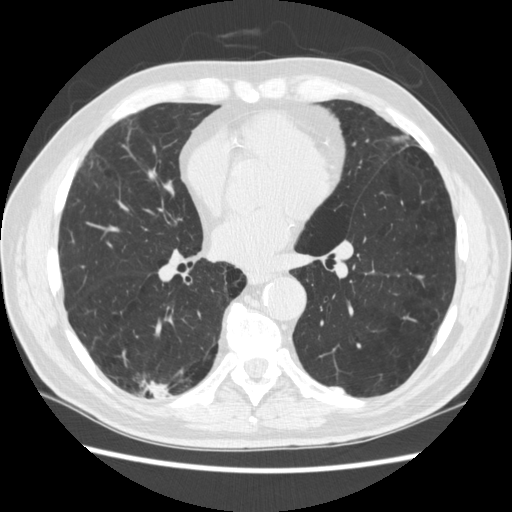
Axial slice from a low-dose chest CT screening exam, third screening round (two years after baseline), lung window (W 1500 / L -600 HU), 1.25 mm slice thickness, standard (soft-tissue) reconstruction kernel (STANDARD), 120 kVp, slice 143 of 266 in the series. Male, age 70 years at enrolment. Former smoker at enrolment.
Expert-annotated lung lesion, bounding box [x1, y1, x2, y2] px = [121, 361, 184, 421]. The screening reader recorded 4 non-calcified nodules or masses ≥4 mm on this exam; which of them this box marks is not recorded.